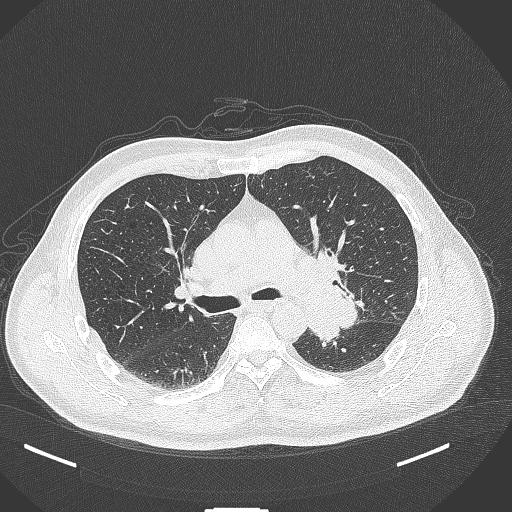
Chest CT, one axial slice; slice 258 of 429 in the series (ordered by position); reconstruction kernel B70f; lung window (W 1500 / L -600 HU); 1 mm slice thickness; 512 × 512 image matrix, field of view 400 × 400 mm. Patient: male, 55 years. From the clinical record (not read from this slice): clinical TNM (as recorded): T3 N0 M1c; histopathological grade: G3.
Structures marked on this image (bounding box drawn by a radiologist):
- lung tumour (recorded histology: adenocarcinoma): bounding box <301,282,368,356> (left, top, right, bottom; pixels)